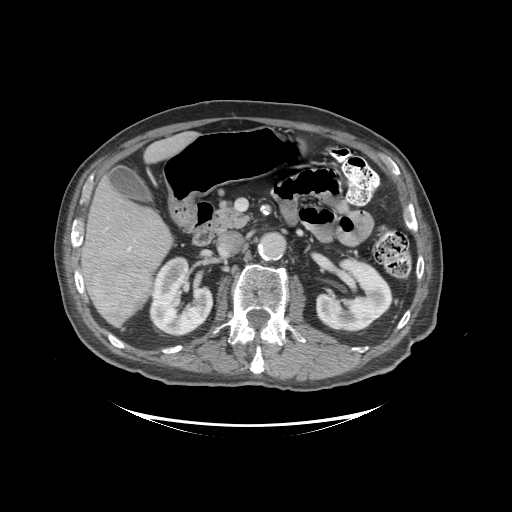
Contrast-enhanced abdominal CT (liver protocol), one axial slice; reconstruction kernel STANDARD; 140 kVp; soft-tissue window (W 400 / L 40 HU); 512 × 512 image matrix, field of view 460 × 460 mm. From the clinical record (not read from this slice): diagnosis: hepatocellular carcinoma (patient treated with transarterial chemoembolisation; whether this scan precedes or follows treatment is not stated here); TNM stage (as recorded): Stage-I; Child-Pugh class: A; tumour nodularity: uninodular.
Annotated regions visible in this slice (semi-automatically segmented with operator editing):
- liver parenchyma outside the tumour (the mass and vessels are separate outlines, so this box may not span the whole liver): box from (x=82, y=132) to (x=194, y=326) px
- mass: (x=86, y=260)–(x=151, y=318)
- liver vessels: (x=128, y=247)–(x=131, y=251)